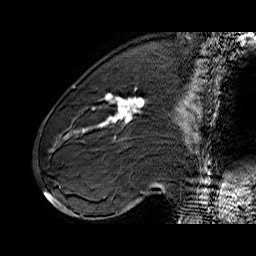
Breast MRI (dynamic contrast-enhanced), one sagittal slice. Slice 22 of 60 in the series (ordered by position). Dynamic contrast-enhanced series, time point 2 of 6 at this slice position (early post-contrast). 1.5 T. TE 6.4 ms, TR 32.9 ms. 4 mm slice thickness. 256 × 256 image matrix, field of view 200 × 200 mm. Female patient. From the clinical record (not read from this slice): setting: breast cancer imaged before/during neoadjuvant chemotherapy; receptor status: HER2-positive.
Outlined on this slice (semi-automatically segmented with operator editing):
- analysis volume of interest (the breast-tissue region the enhancement analysis was run in; not a lesion): bounding box <71,80,155,146> (left, top, right, bottom; pixels)
- tumour enhancement mask (voxels above the 100 % enhancement threshold inside the analysis volume of interest): <77,94,145,133>